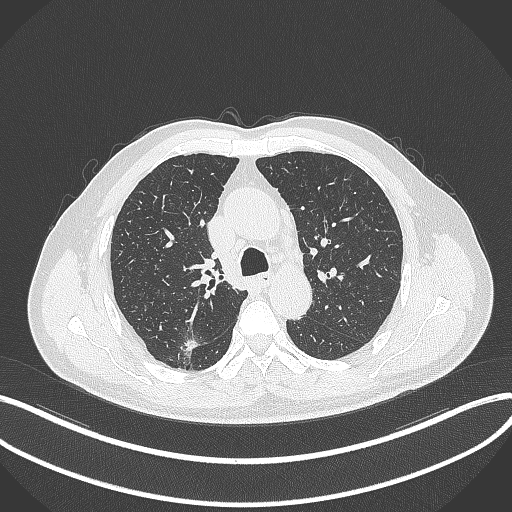
Chest CT, one axial slice. Slice 253 of 359 in the series (ordered by position). 120 kVp. Lung window (W 1500 / L -600 HU). 1 mm slice thickness. 512 × 512 image matrix, field of view 400 × 400 mm. Male patient, age 69 years. Case-level facts recorded for this patient, not image findings: clinical TNM (as recorded): T1b N0 M0.
Structures marked on this image (rectangle marked by the reading radiologist):
- lung tumour (recorded histology: adenocarcinoma): box from (x=182, y=338) to (x=201, y=358) px